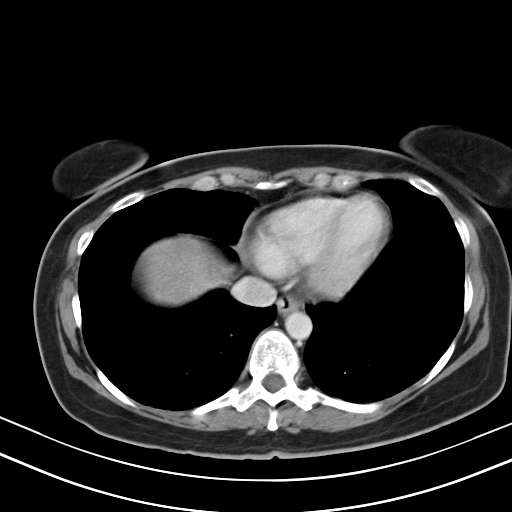
Contrast-enhanced abdominal CT, one axial slice; slice 44 of 47 in the series (ordered by position); reconstruction kernel B40s; intravenous contrast given; soft-tissue window (W 400 / L 40 HU); 5 mm slice thickness; 512 × 512 image matrix, field of view 350 × 350 mm. Female patient. From the clinical record (not read from this slice): diagnosis: colorectal cancer liver metastases, imaged before liver resection; multiple liver metastases: no; largest metastasis: 3.5 cm; disease in both lobes: no.
Outlined on this slice (outlined manually by an expert reader):
- liver: box from (x=140, y=242) to (x=223, y=304) px
- planned liver remnant (the part of the liver to remain after resection): (x=140, y=242)–(x=223, y=305)